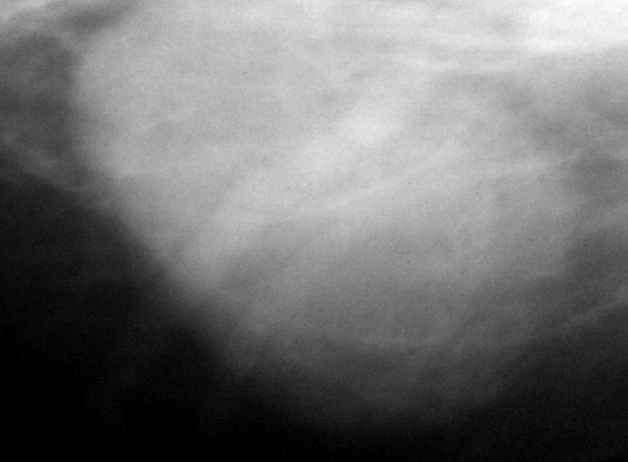
Crop from a digitized film mammogram around one marked abnormality; right breast; MLO view; BI-RADS breast density category 2 (scale 1–4).
Finding: mass, shape oval, margins circumscribed; BI-RADS assessment category 3; subtlety rating 5 on a 1 (subtle) to 5 (obvious) scale; pathology result (as recorded, not read from the image): benign.